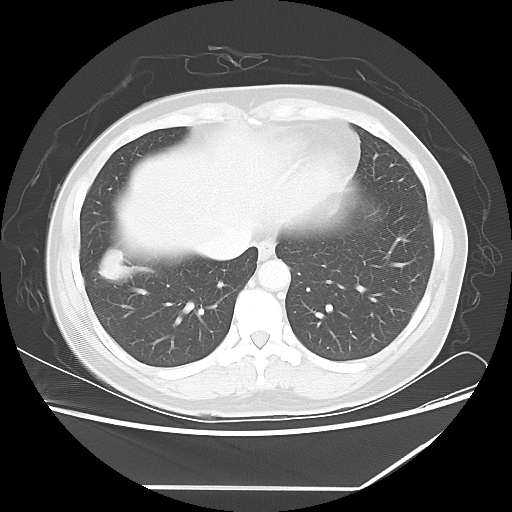
Chest CT, one axial slice. Slice 19 of 60 in the series (ordered by position). Reconstruction kernel LUNG. 100 kVp. Lung window (W 1500 / L -600 HU). 5 mm slice thickness. 512 × 512 image matrix. Female patient, age 42 years. Case-level facts recorded for this patient, not image findings: clinical TNM (as recorded): T2 N1 M0.
Structures marked on this image (bounding box drawn by a radiologist):
- lung tumour (recorded histology: adenocarcinoma): bounding box [x1, y1, x2, y2] px = [91, 245, 130, 287]